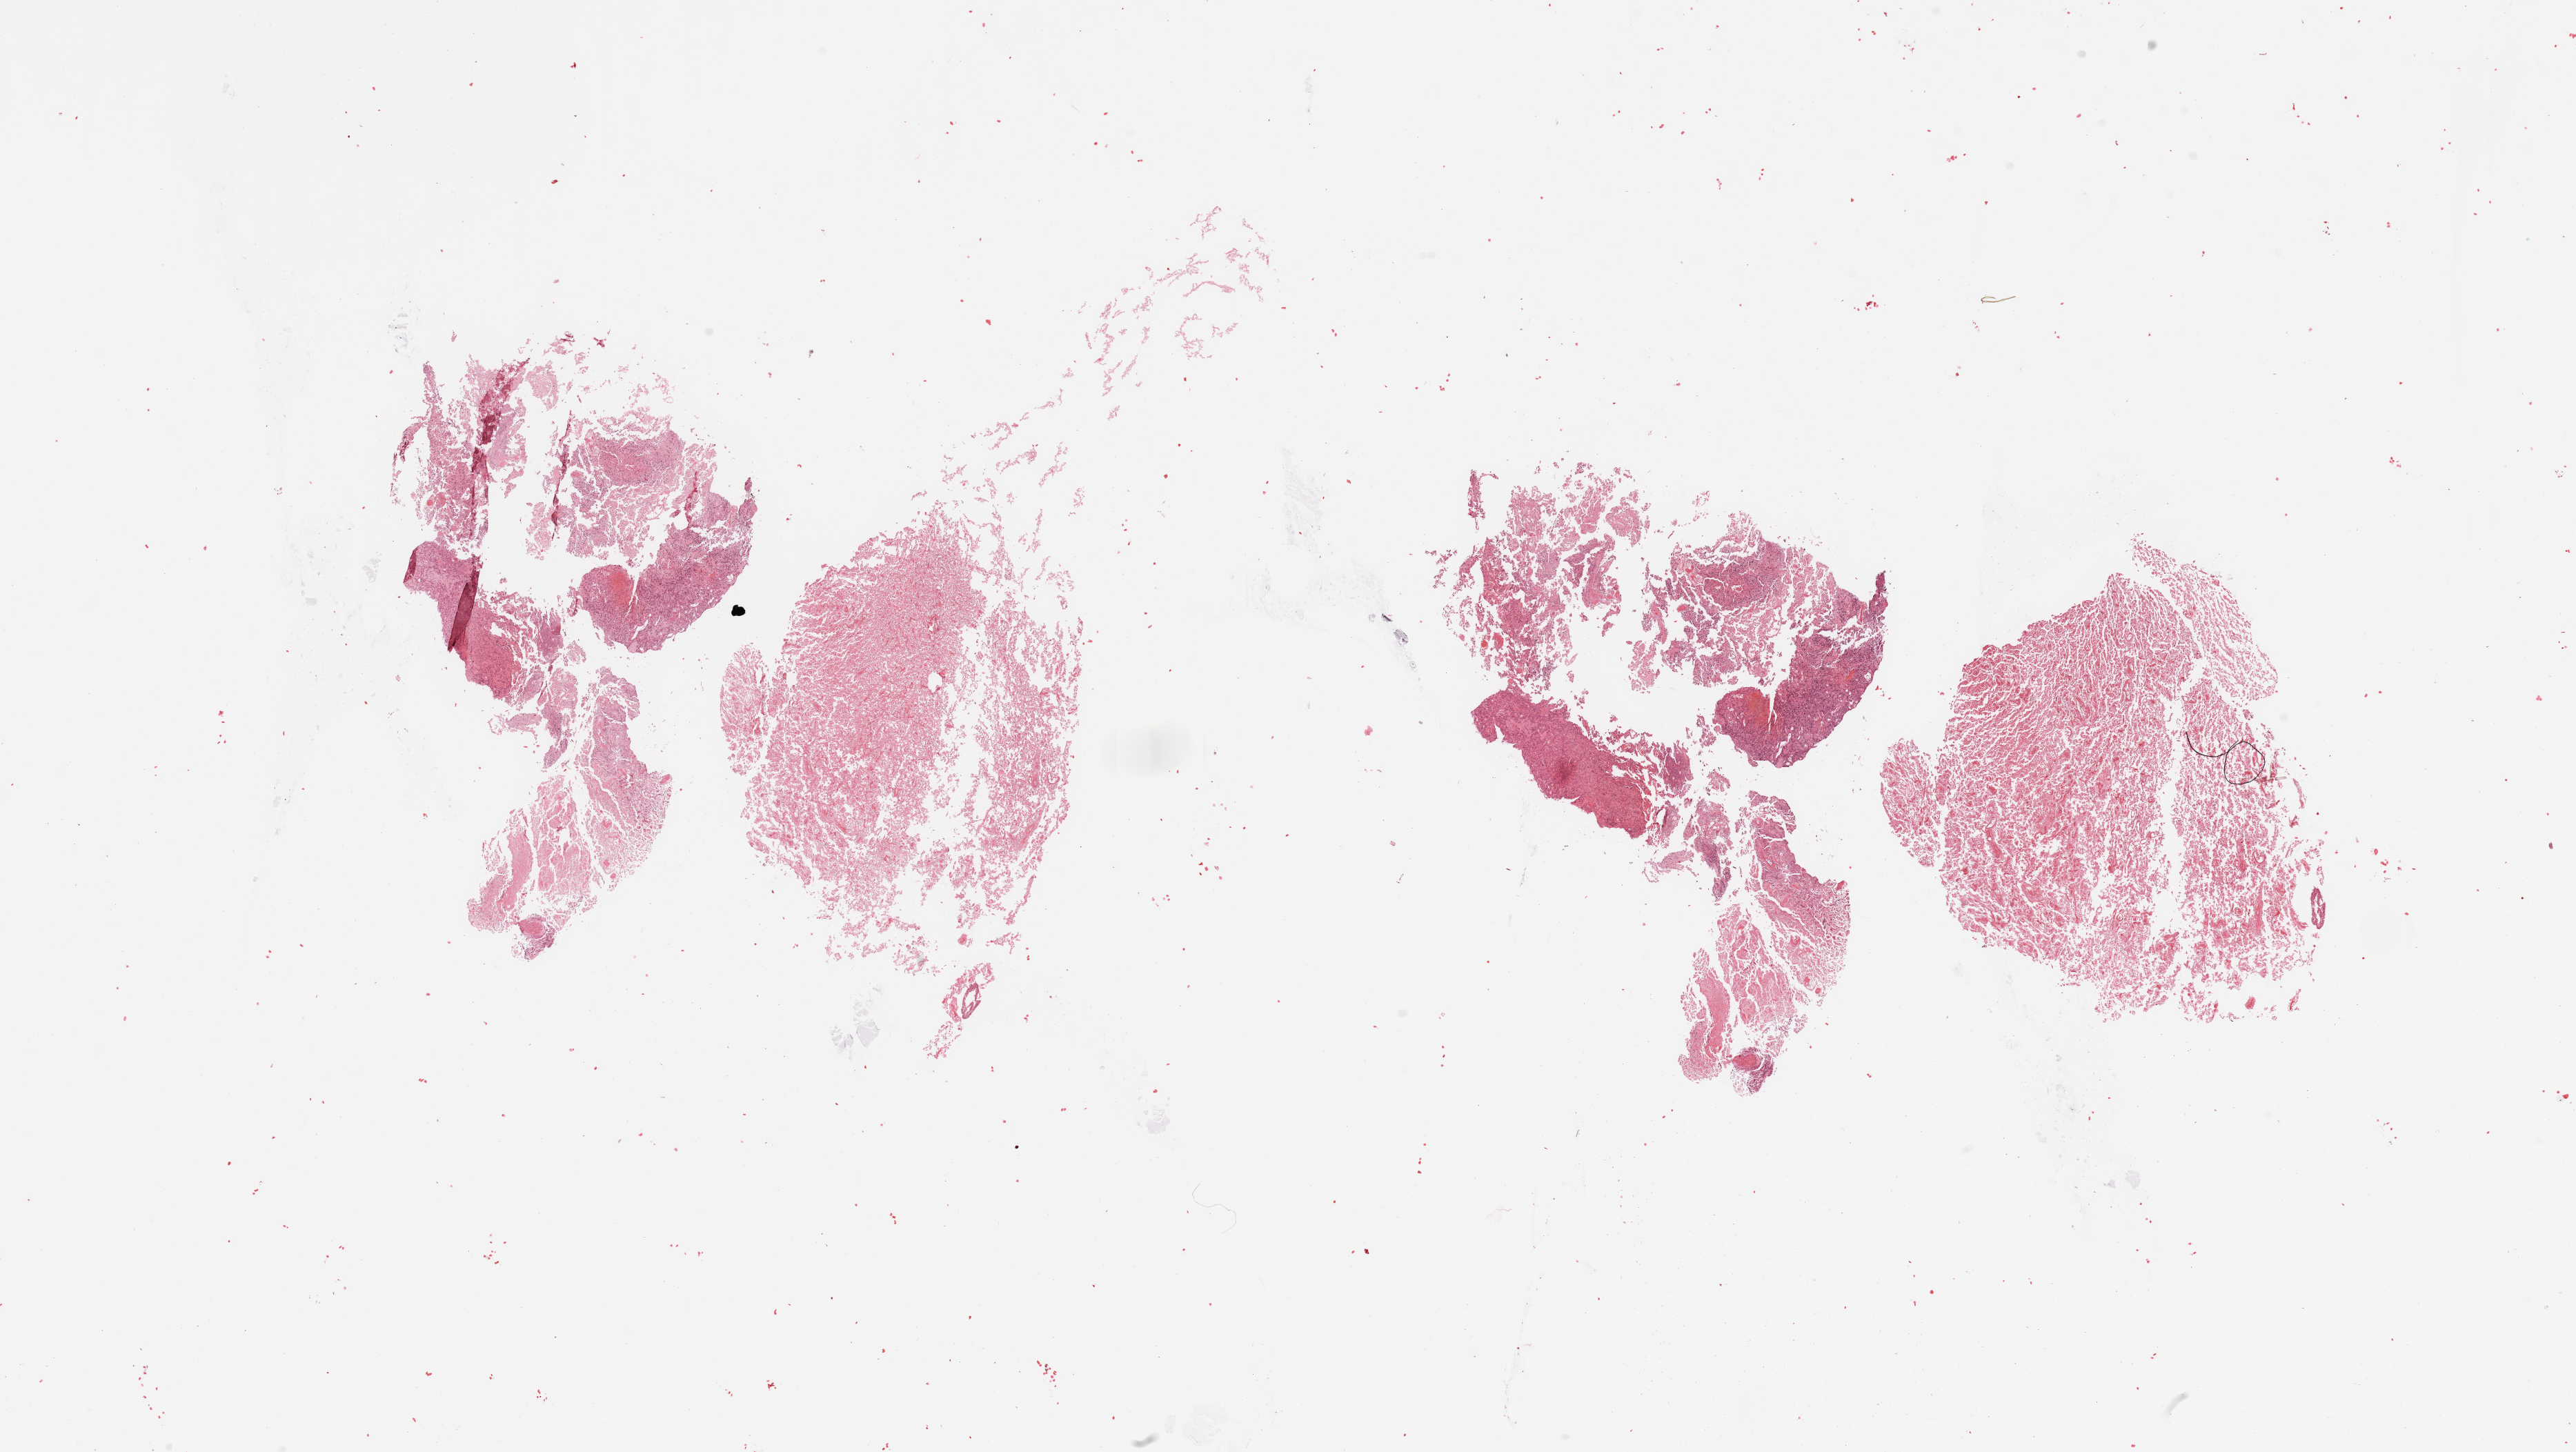
Digitized H&E-stained tissue section (whole slide), whole scanned area (about 29.5 x 16.6 mm, acquisition: 20x scan) shown as a low-resolution overview. Brain, tumour tissue. Patient: male, age 49 years.
* histologic diagnosis: Glioblastoma
* primary tumour site (as recorded): temporal lobe